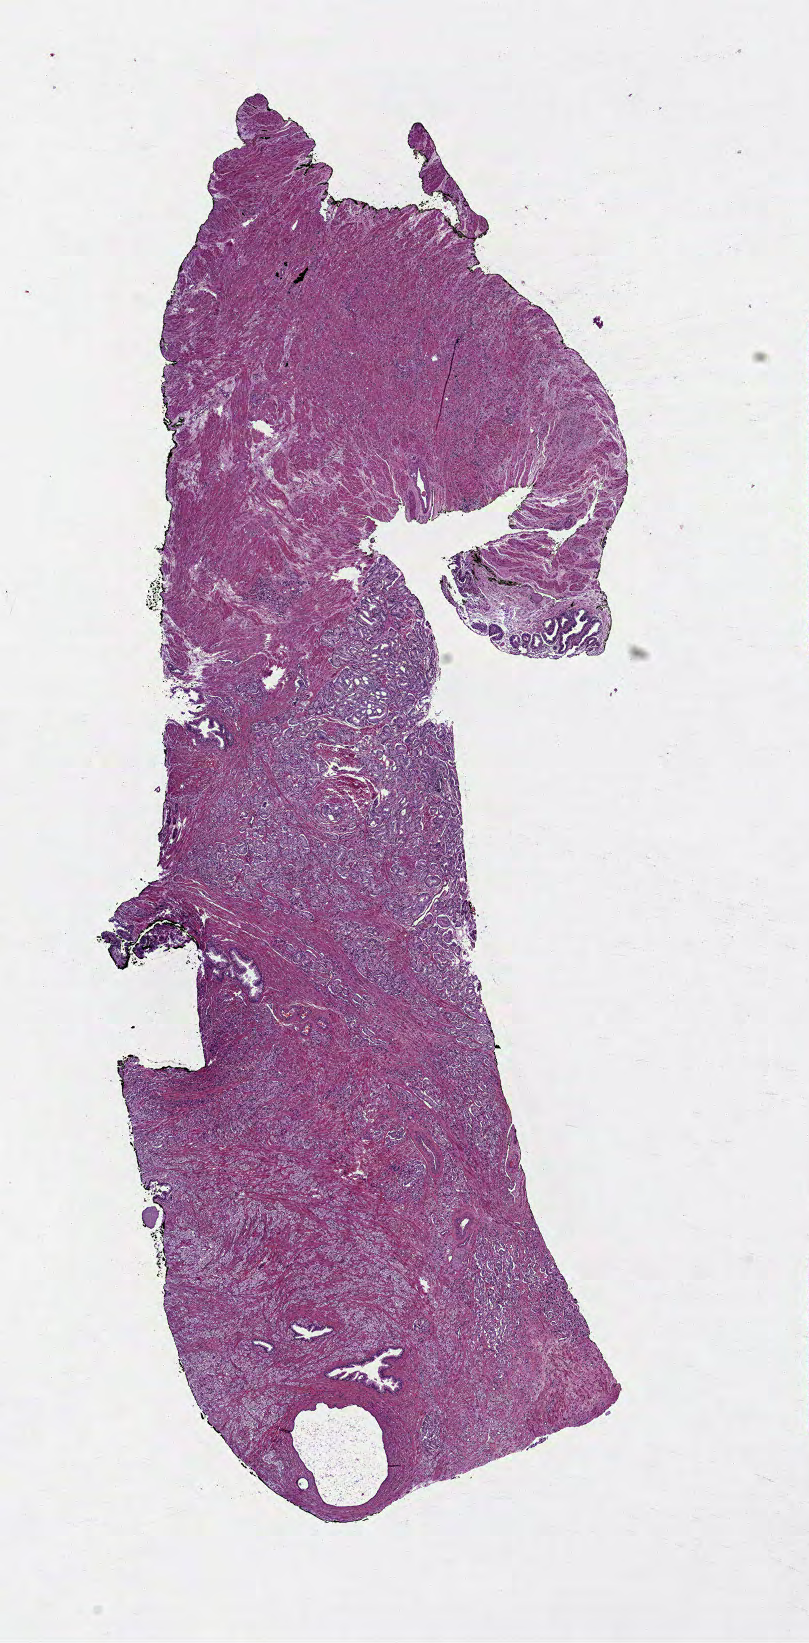
Whole-slide histology image, Hematoxylin and eosin (H&E) stained — whole scanned area (about 6.5 x 13.3 mm) shown as a low-resolution overview, FFPE section, primary tumour sample from the prostate. Male patient; age at initial diagnosis 60 years. Gleason score: 9 (4+5).
Histologic diagnosis: Acinar cell carcinoma (prostate gland).